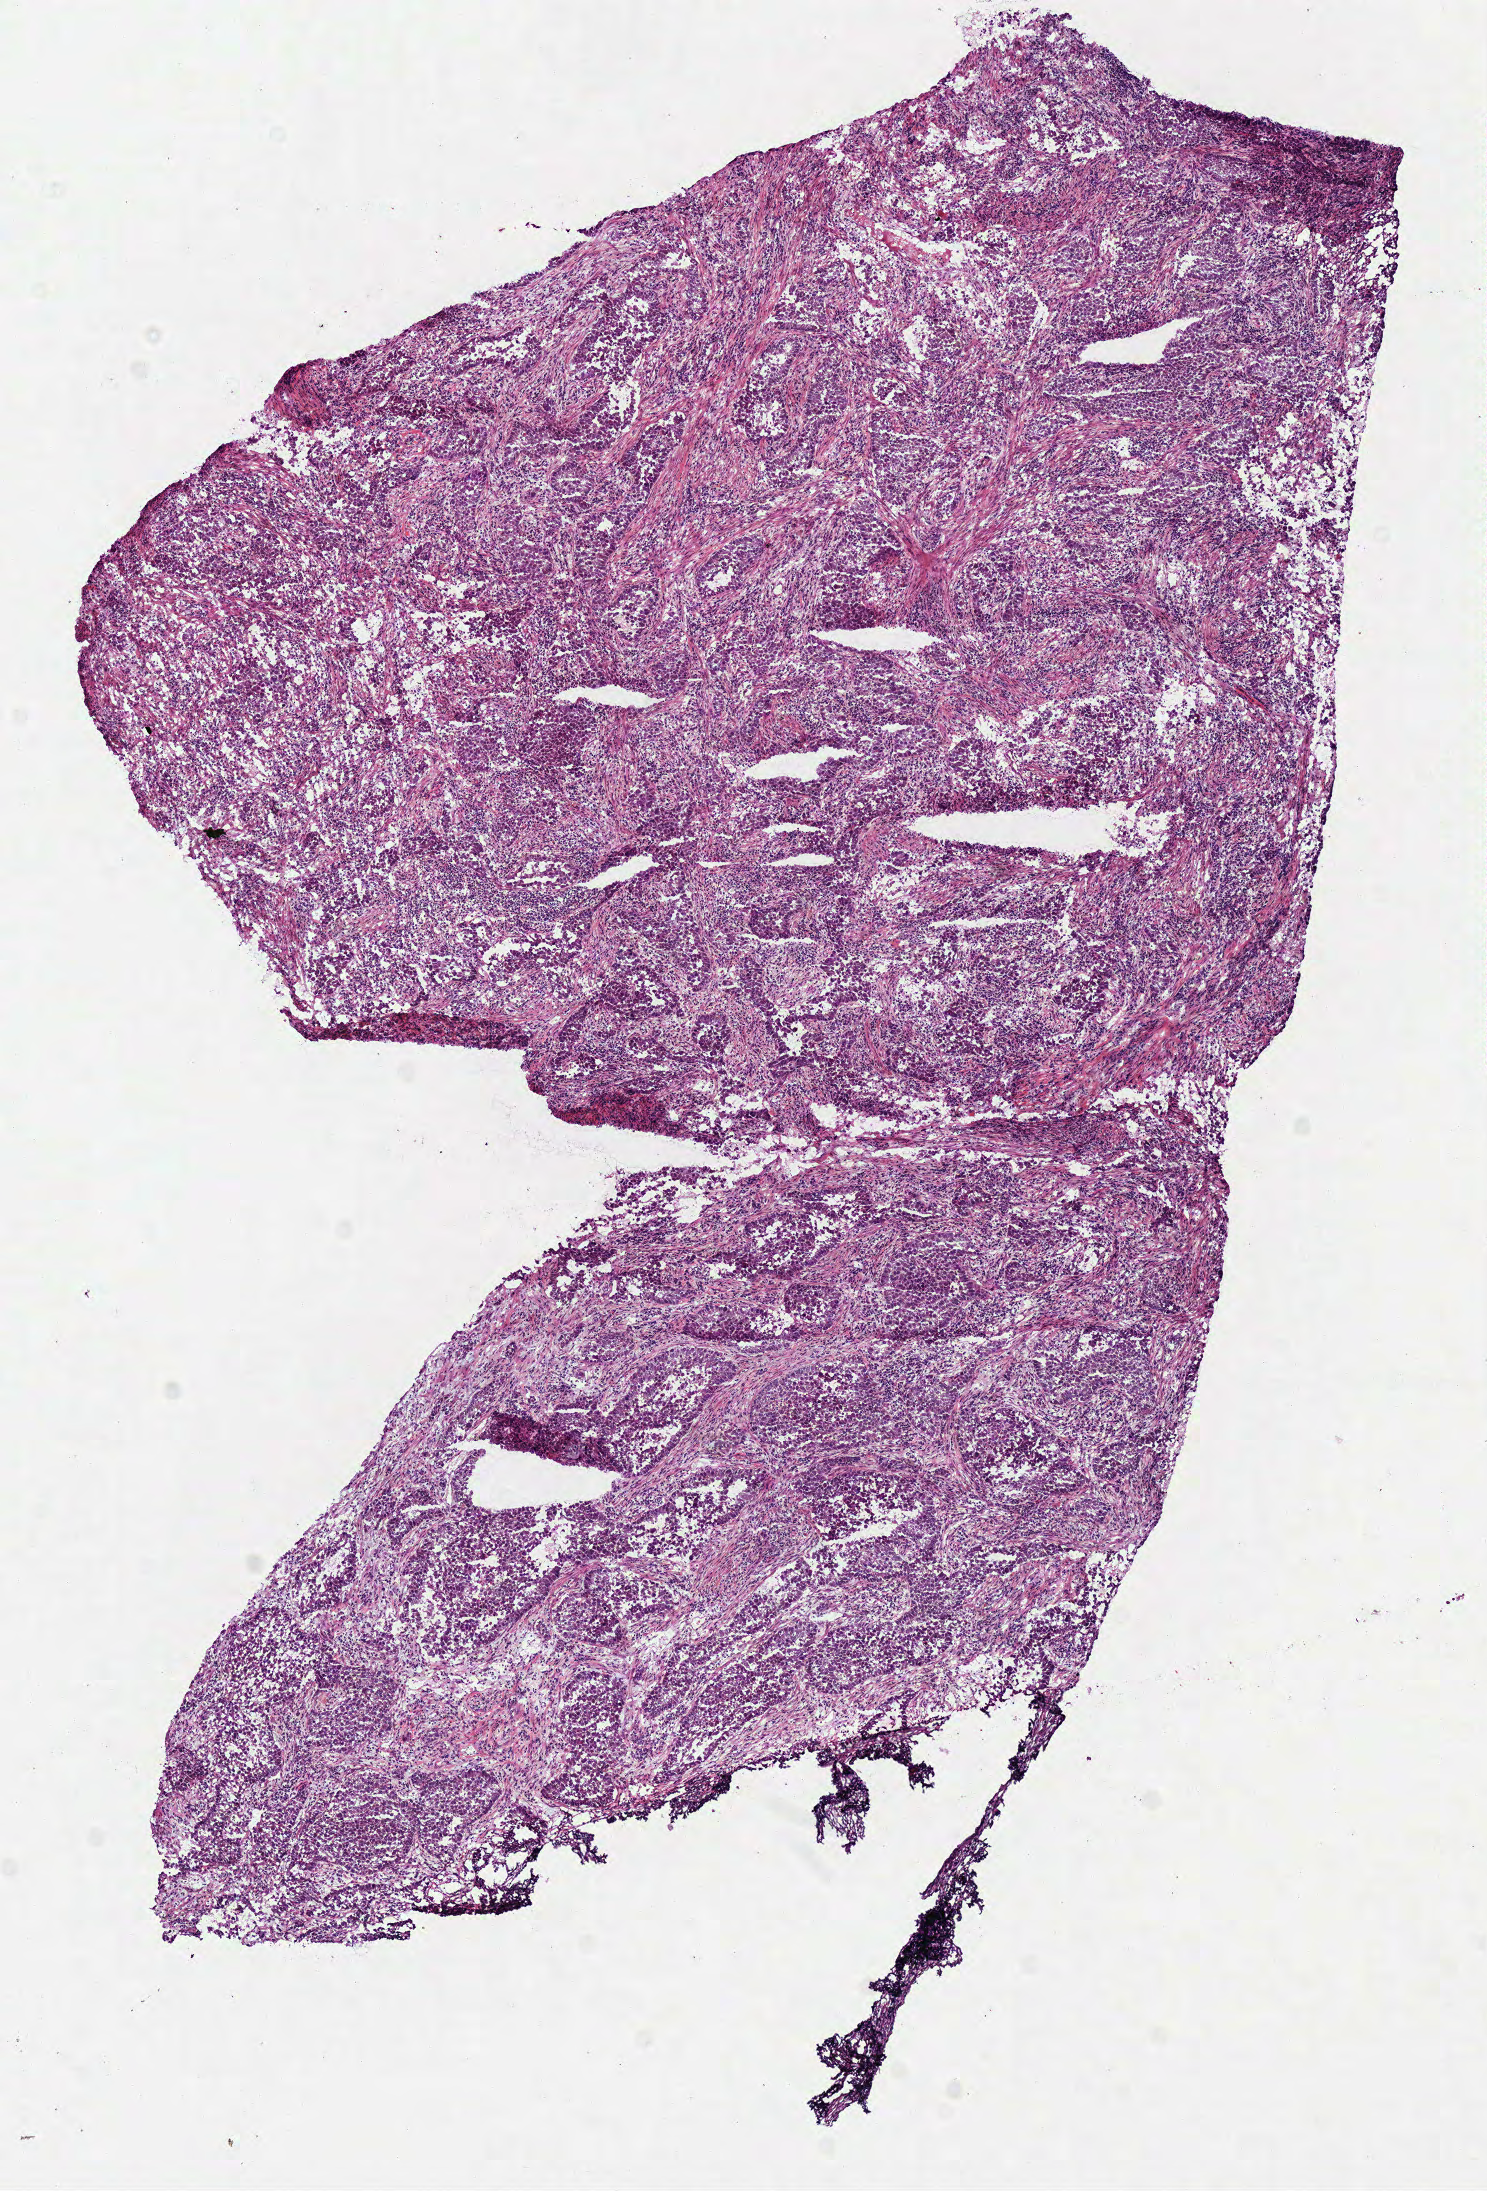
Digitized Hematoxylin and eosin (H&E) stained tissue section (whole slide), a low-resolution overview of the entire scanned area, about 5.9 x 8.6 mm (slide scanned at 40x), frozen section from the bottom of the tissue portion, primary tumour sample from the lung. Female patient. Composition of this section per pathologist review: tumour cells 100%, tumour nuclei 60%, normal cells 0%, stromal cells 0%, necrosis 0%. Inflammatory infiltration, as recorded: lymphocyte infiltration 20%, monocyte infiltration 2%, neutrophil infiltration 2%.
Diagnosis: Adenocarcinoma, NOS. AJCC pathologic stage: IB (6th edition).